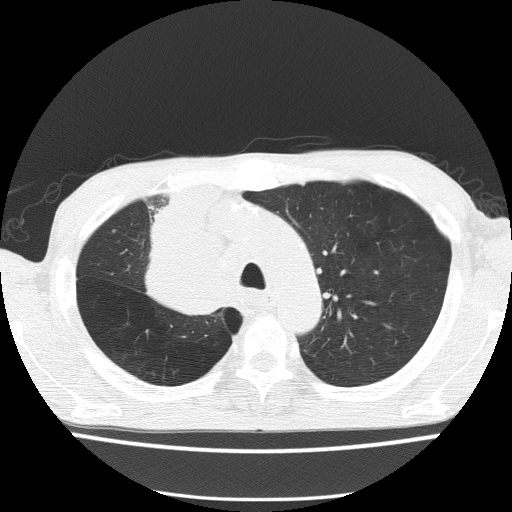
Axial slice from a low-dose chest CT screening exam; baseline annual screen; lung window (W 1500 / L -600 HU); 2 mm slice thickness; lung (sharp) reconstruction kernel (FC51); 120 kVp; 512 × 512 image matrix. Male, age 59 years at enrolment. Former smoker at enrolment.
Expert-annotated lung lesion, box from (x=133, y=234) to (x=238, y=326) px. The screening reader recorded 5 non-calcified nodules or masses ≥4 mm on this exam (left upper lobe, left upper lobe, left upper lobe, right middle lobe, right lower lobe); which of them this box marks is not recorded. Official screen result: positive, change unspecified: nodule(s) >= 4 mm or enlarging nodule(s), mass(es), or other non-specific abnormalities suspicious for lung cancer. Lung cancer was diagnosed 72 days after this screen: squamous cell carcinoma, NOS, right upper lobe, moderately differentiated (G2), stage IV (AJCC 6th edition).